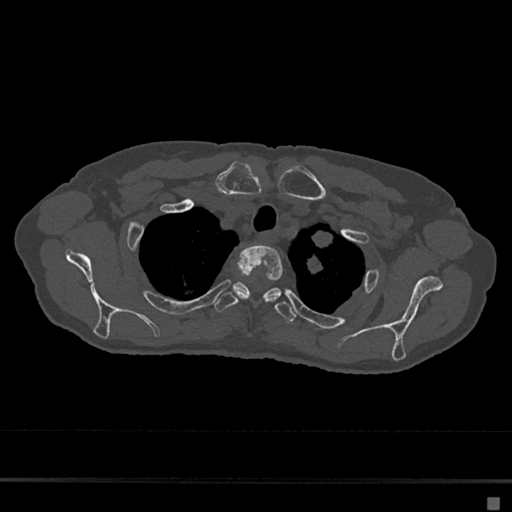
CT including the spine, one axial slice; position 561 of 797 along the scan axis; reconstruction kernel Br40s/3; 120 kVp; bone window (W 1800 / L 400 HU); 0.5 mm slice thickness; 512 × 512 image matrix, field of view 360 × 360 mm. Female patient, age 68 years. Case-level facts recorded for this patient, not image findings: primary cancer: renal.
Annotated regions visible in this slice (semi-automatically segmented with operator editing):
- T2 vertebra: bounding box <233,245,283,303> (left, top, right, bottom; pixels)
- T3 vertebra: <213,282,297,323>